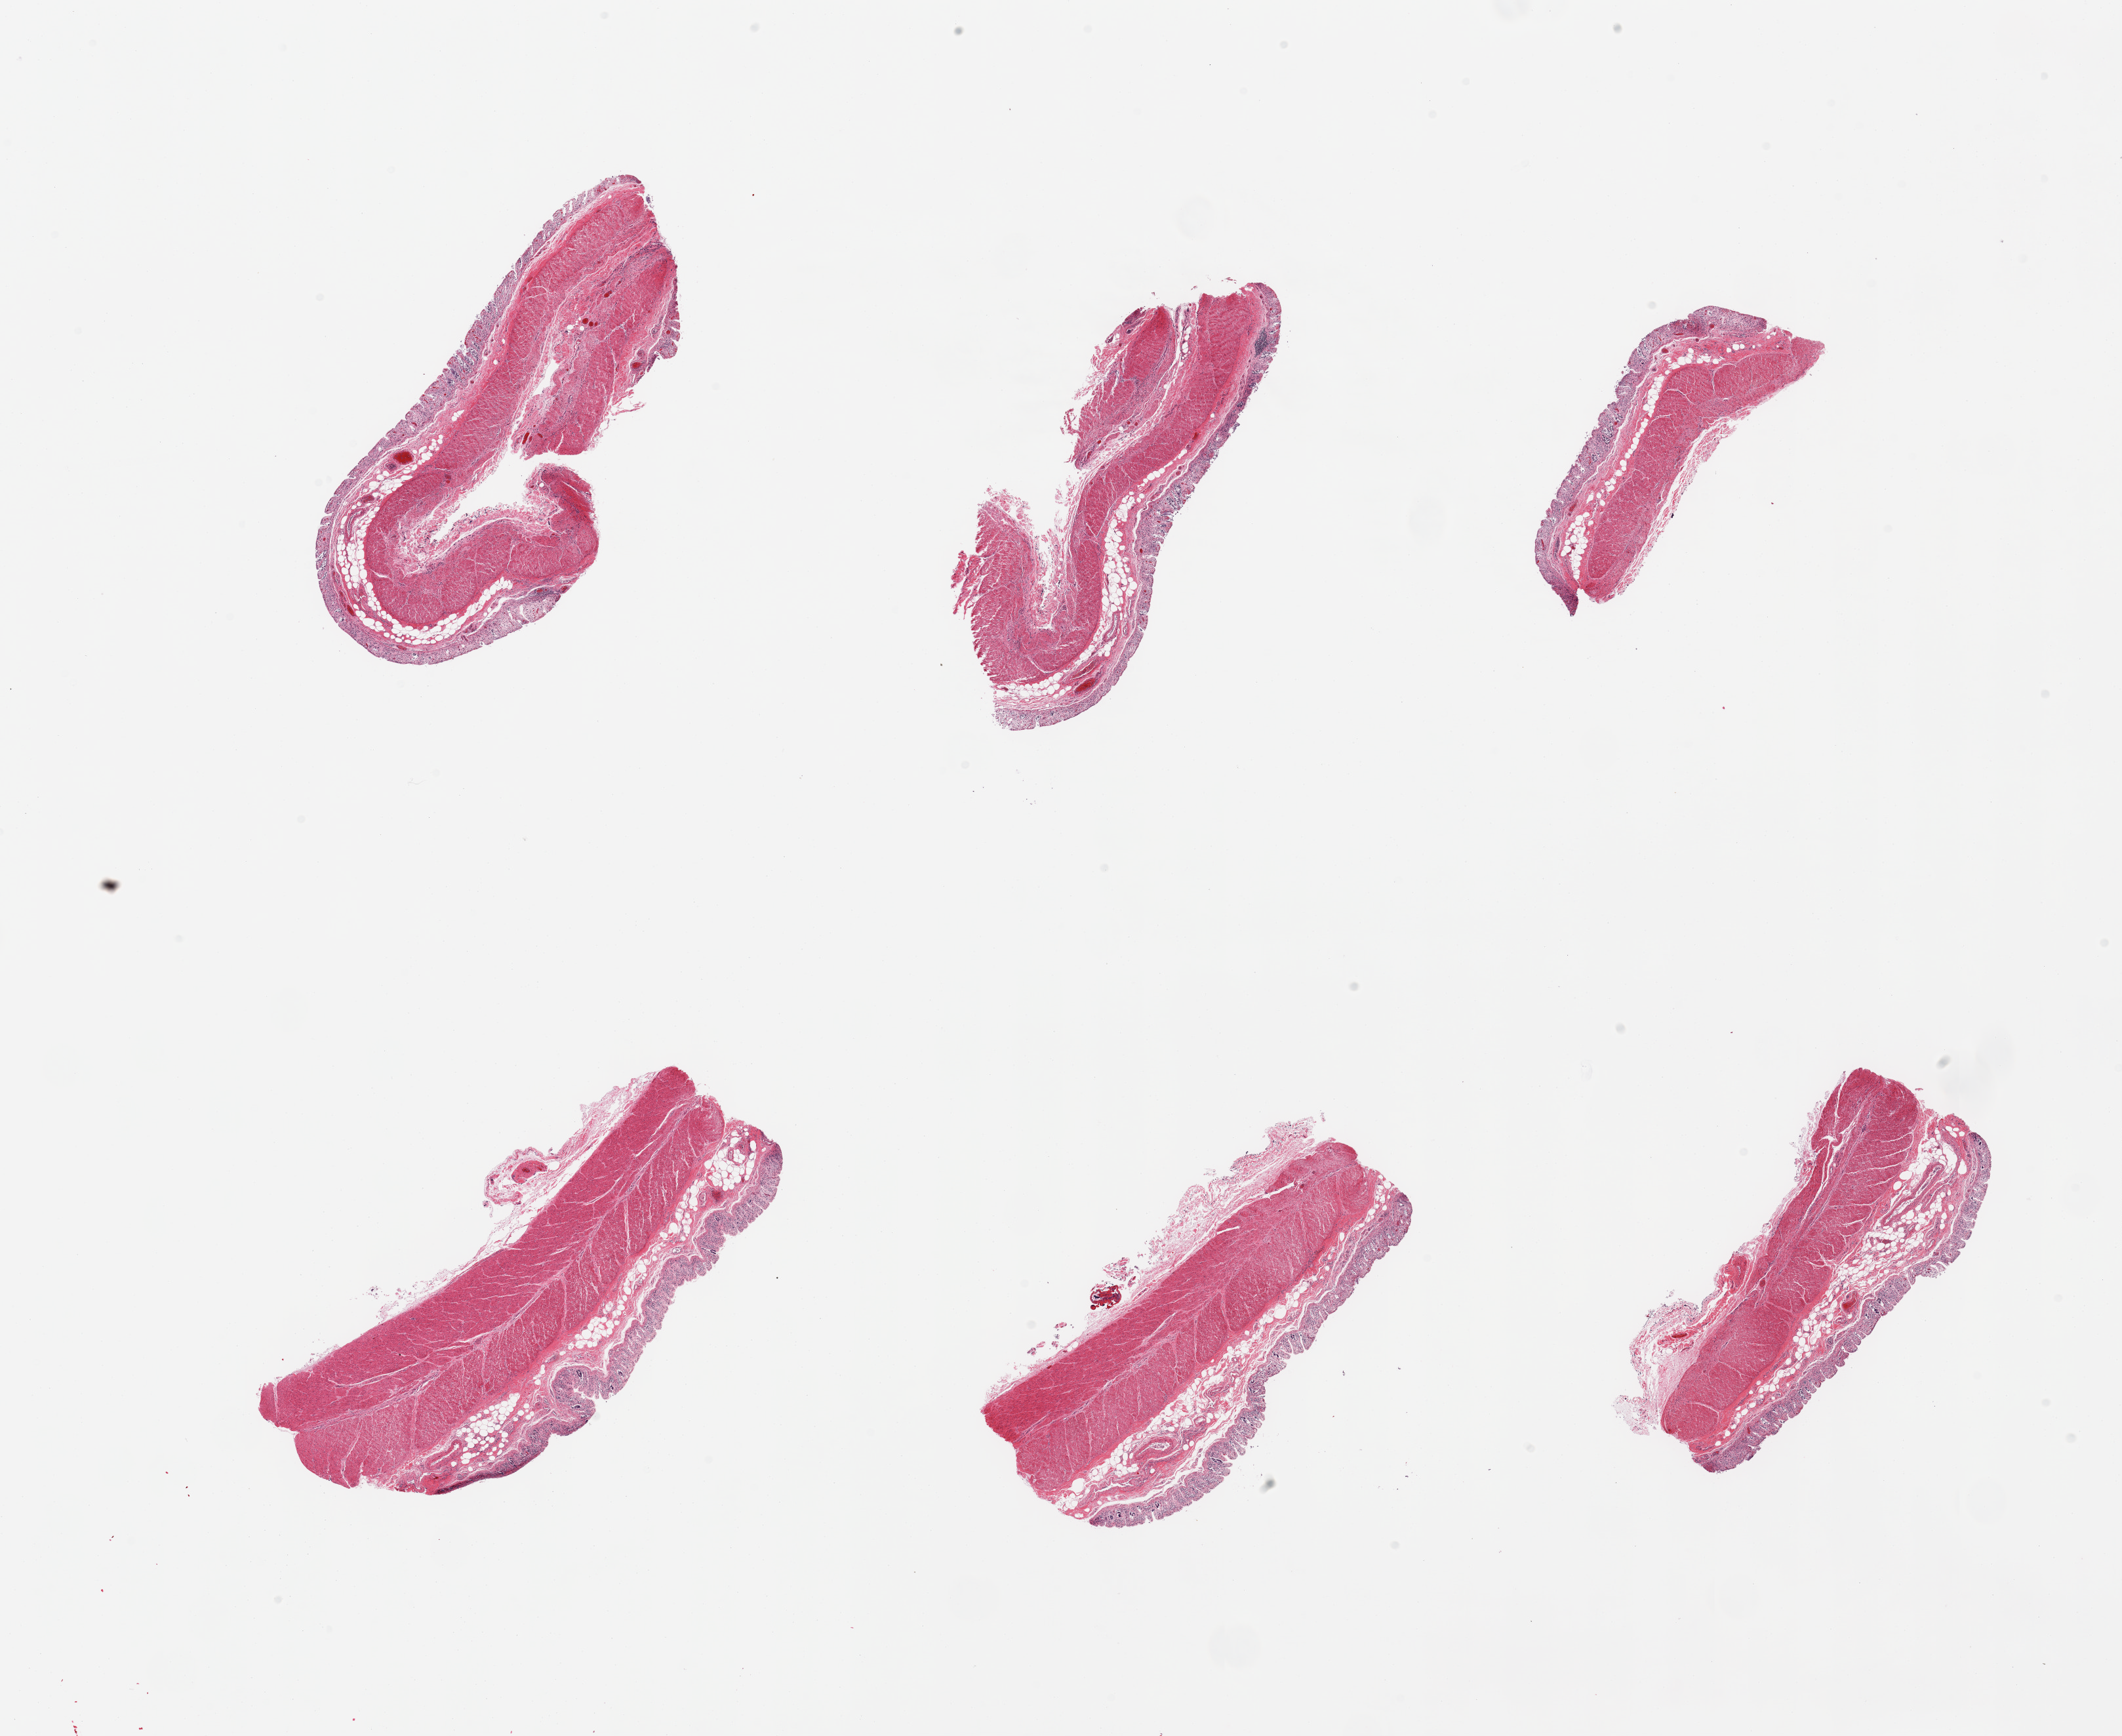
Digitized hematoxylin and eosin (H&E)-stained section, brightfield, low-resolution overview of the scanned area, about 25.6 x 20.9 mm (from a 20x scan). PAXgene-fixed, paraffin-embedded tissue. Sampled site (target tissue): transverse colon. Donor tissue sample. Male donor.
Review note (as recorded): 6 pieces, mucosa with advanced autolysis.